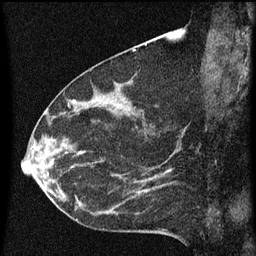
Breast MRI (dynamic contrast-enhanced), one sagittal slice; position 27 of 60 along the scan axis; dynamic contrast-enhanced series, image 2 of 3 at this slice position (ordered by acquisition); 1.5 T; TE 4.2 ms, TR 8 ms; 2 mm slice thickness; 256 × 256 image matrix, field of view 180 × 180 mm. Patient: female, 55 years.
Annotated regions visible in this slice (semi-automatic segmentation, software-assisted and operator-edited):
- analysis volume of interest (the breast-tissue region the enhancement analysis was run in; not a lesion): box from (x=51, y=156) to (x=145, y=217) px
- tumour enhancement mask (voxels above the 70 % enhancement threshold inside the analysis volume of interest): (x=51, y=168)–(x=145, y=209)